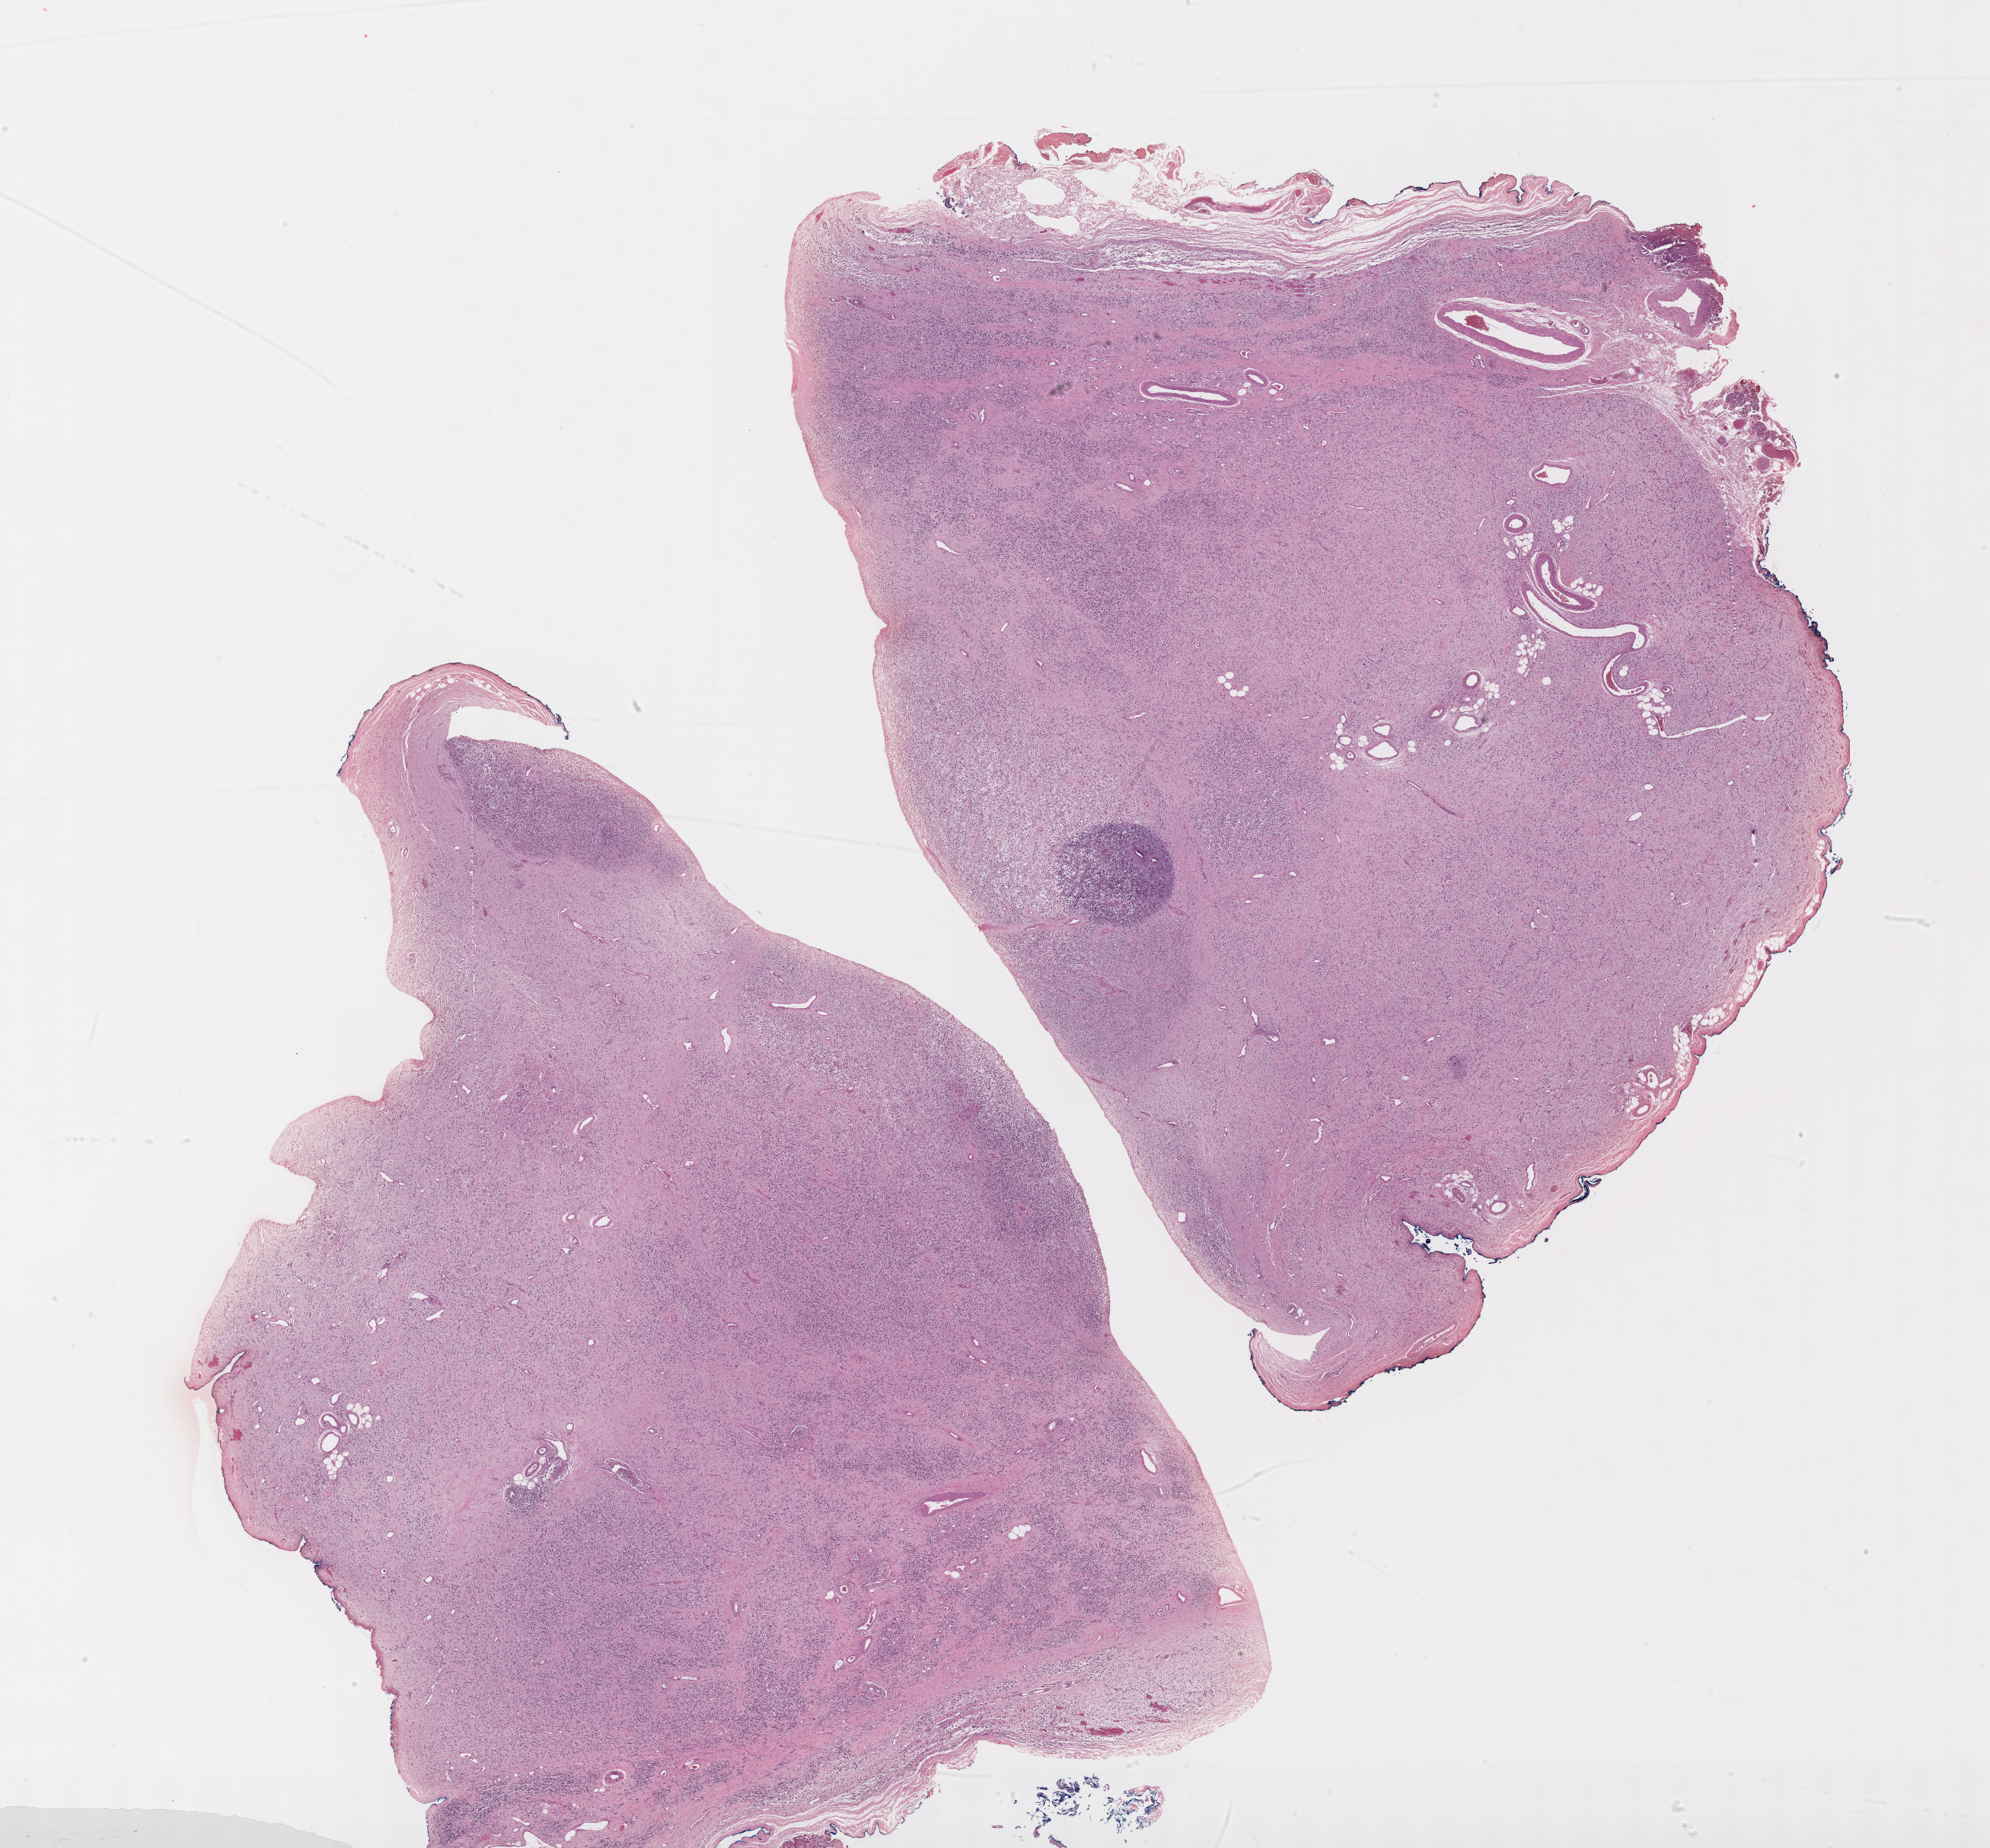
Hematoxylin and eosin (H&E) whole-slide image of tumor tissue — a low-resolution overview of the entire scanned area, about 21.1 x 19.6 mm. FFPE section. Patient: male, age 19.5 years at diagnosis.
• stage (as recorded): 1
• diagnosis: rhabdomyosarcoma; histological classification: embryonal rhabdomyosarcoma
• metastatic status at presentation (as recorded): non-metastatic